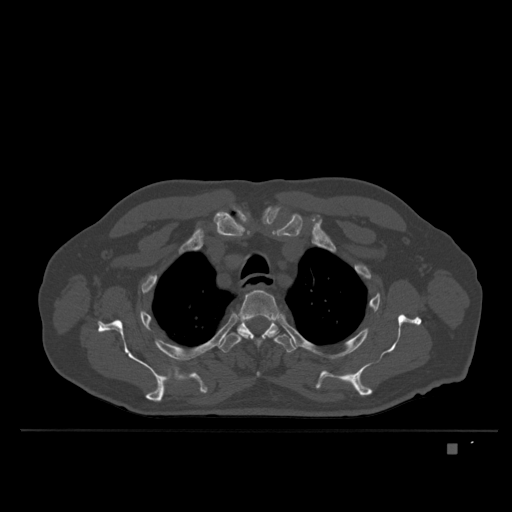
CT including the spine, one axial slice; slice 295 of 435 in the series (ordered by position); bone window (W 1800 / L 400 HU); 1.5 mm slice thickness; 512 × 512 image matrix, field of view 434 × 434 mm. Patient: male, 73 years. Case-level facts recorded for this patient, not image findings: primary cancer: skin.
Structures marked on this image (semi-automatically segmented with operator editing):
- T3 vertebra: bounding box (x1, y1, x2, y2) in pixels: (237, 290, 281, 377)
- T4 vertebra: (218, 321, 297, 354)